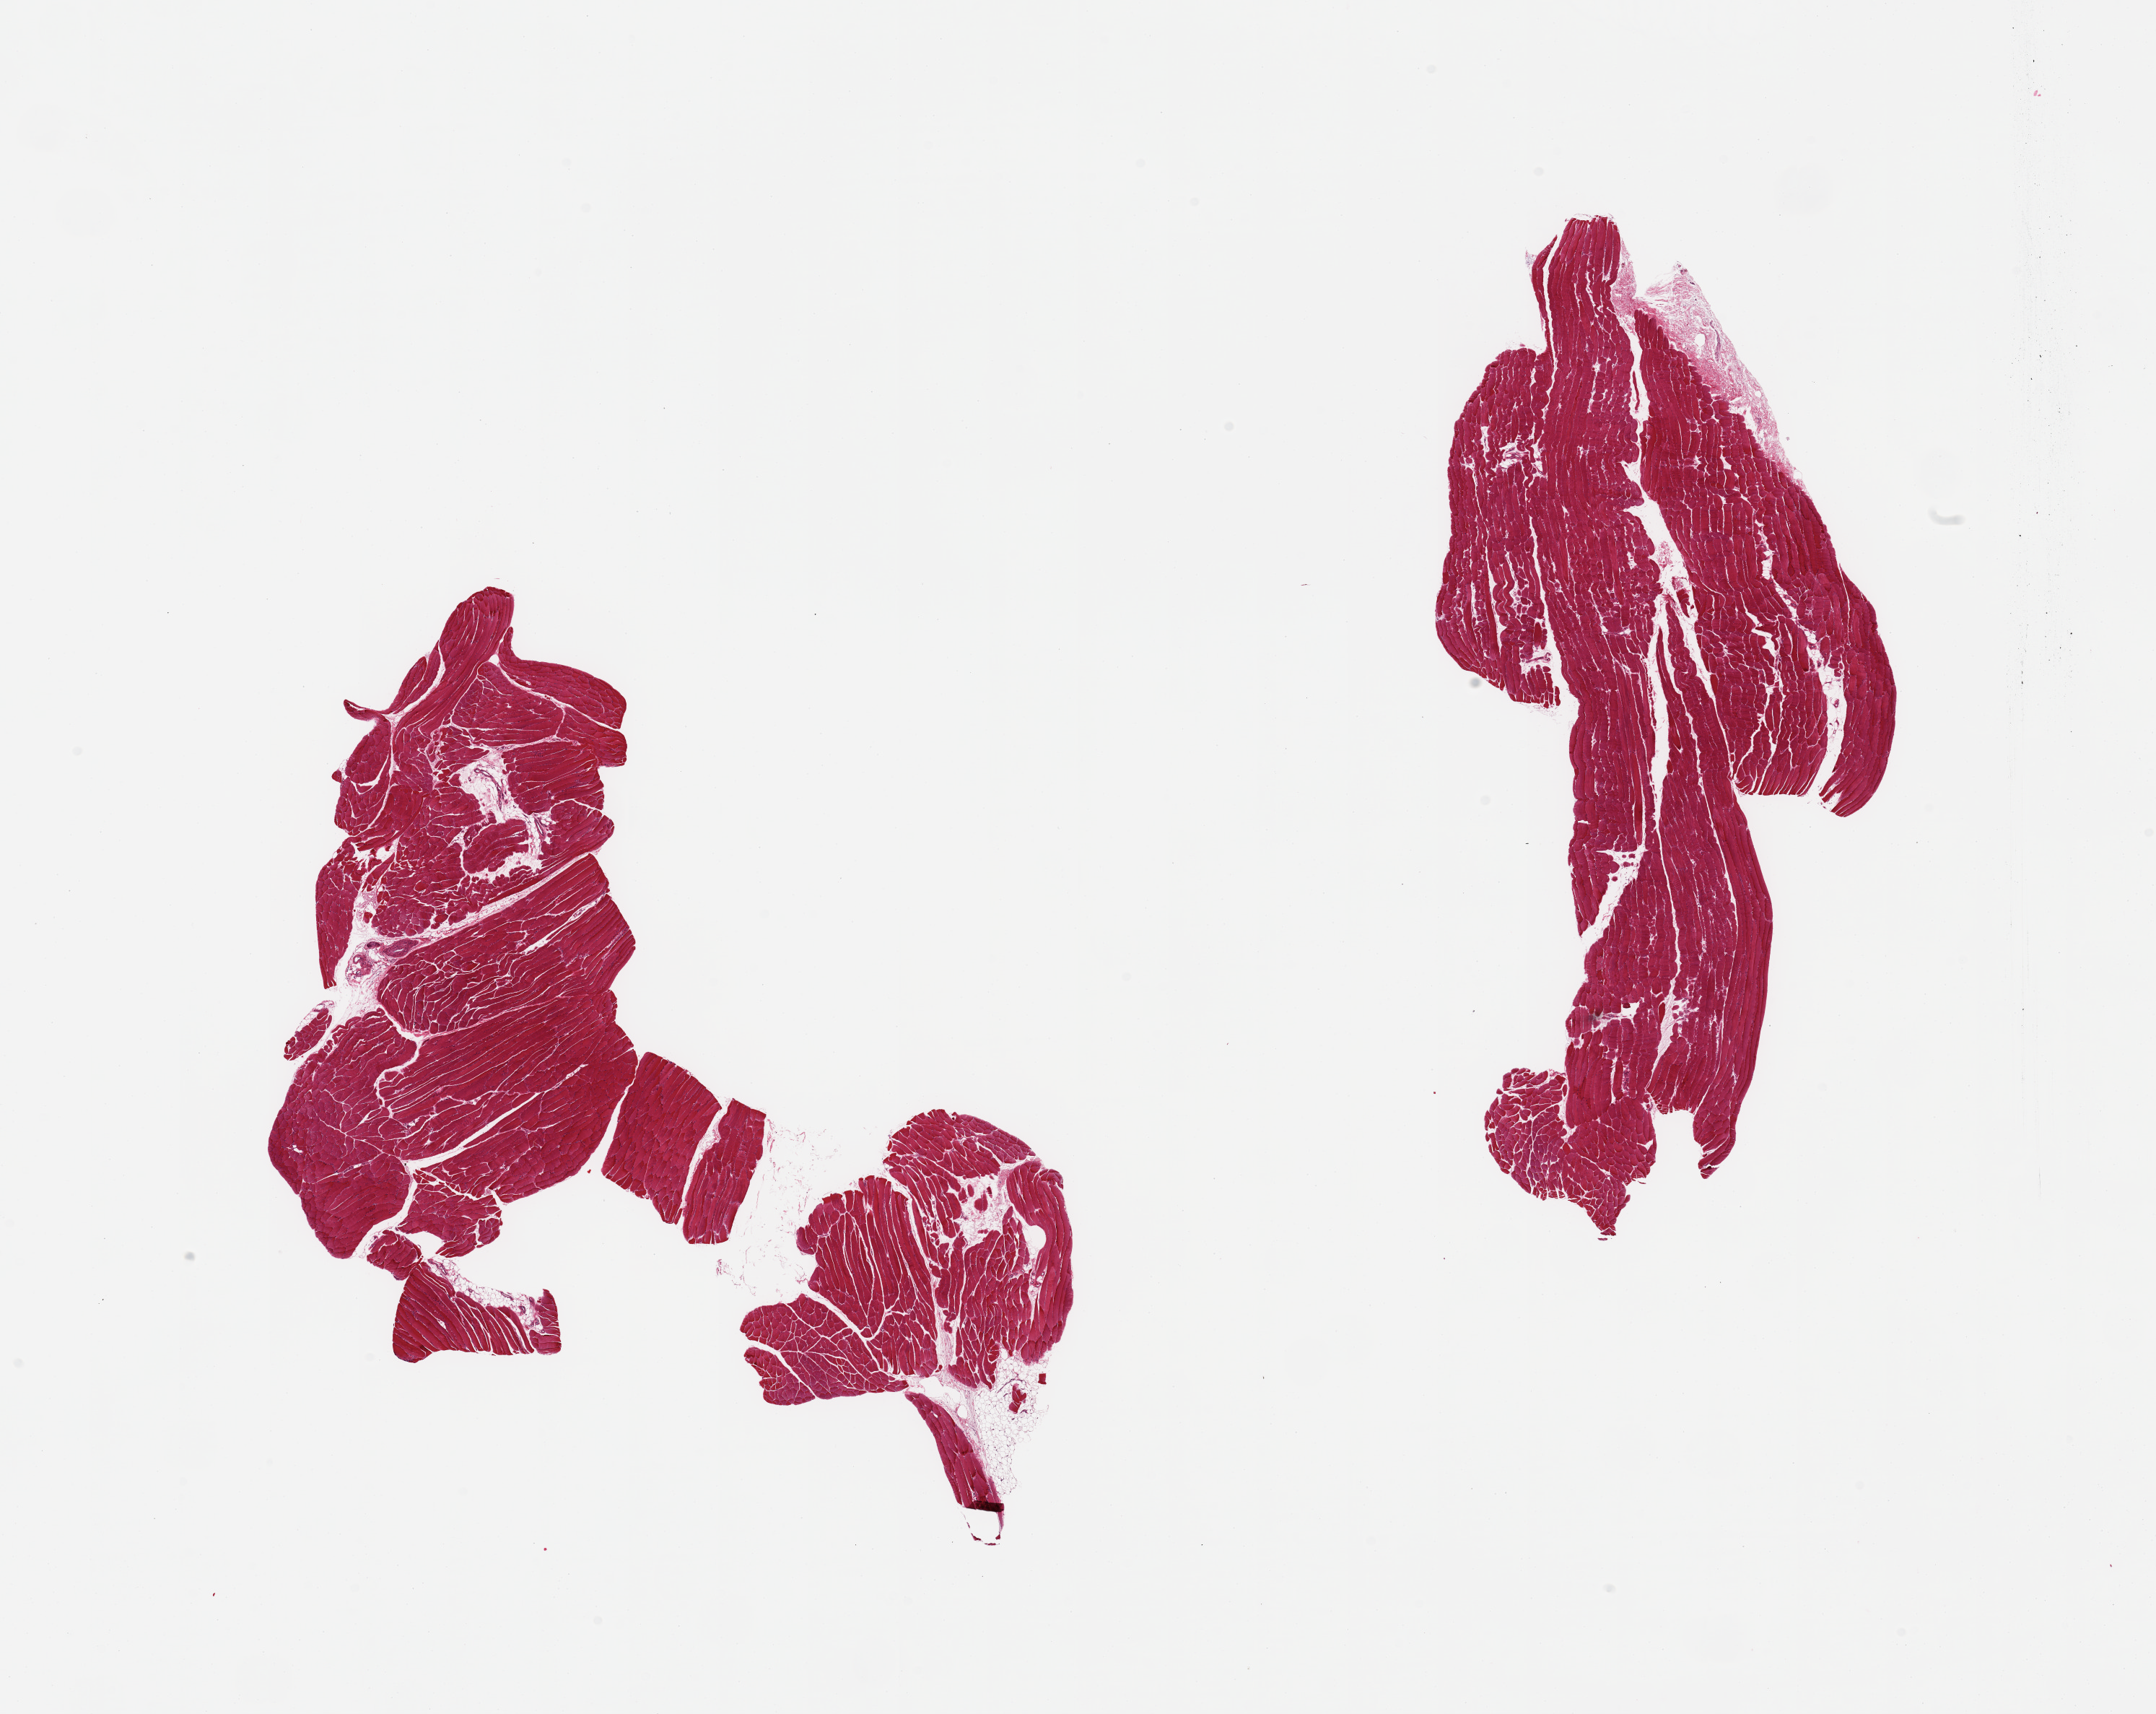
Whole-slide image, H&E stain — whole scanned area (about 23.6 x 18.8 mm) shown as a low-resolution overview; PAXgene-fixed, paraffin-embedded tissue; target tissue: skeletal muscle; donor tissue sample. Donor sex: female.
Review note (as recorded): 2 pieces; includes 5-10% attached and internal fat.